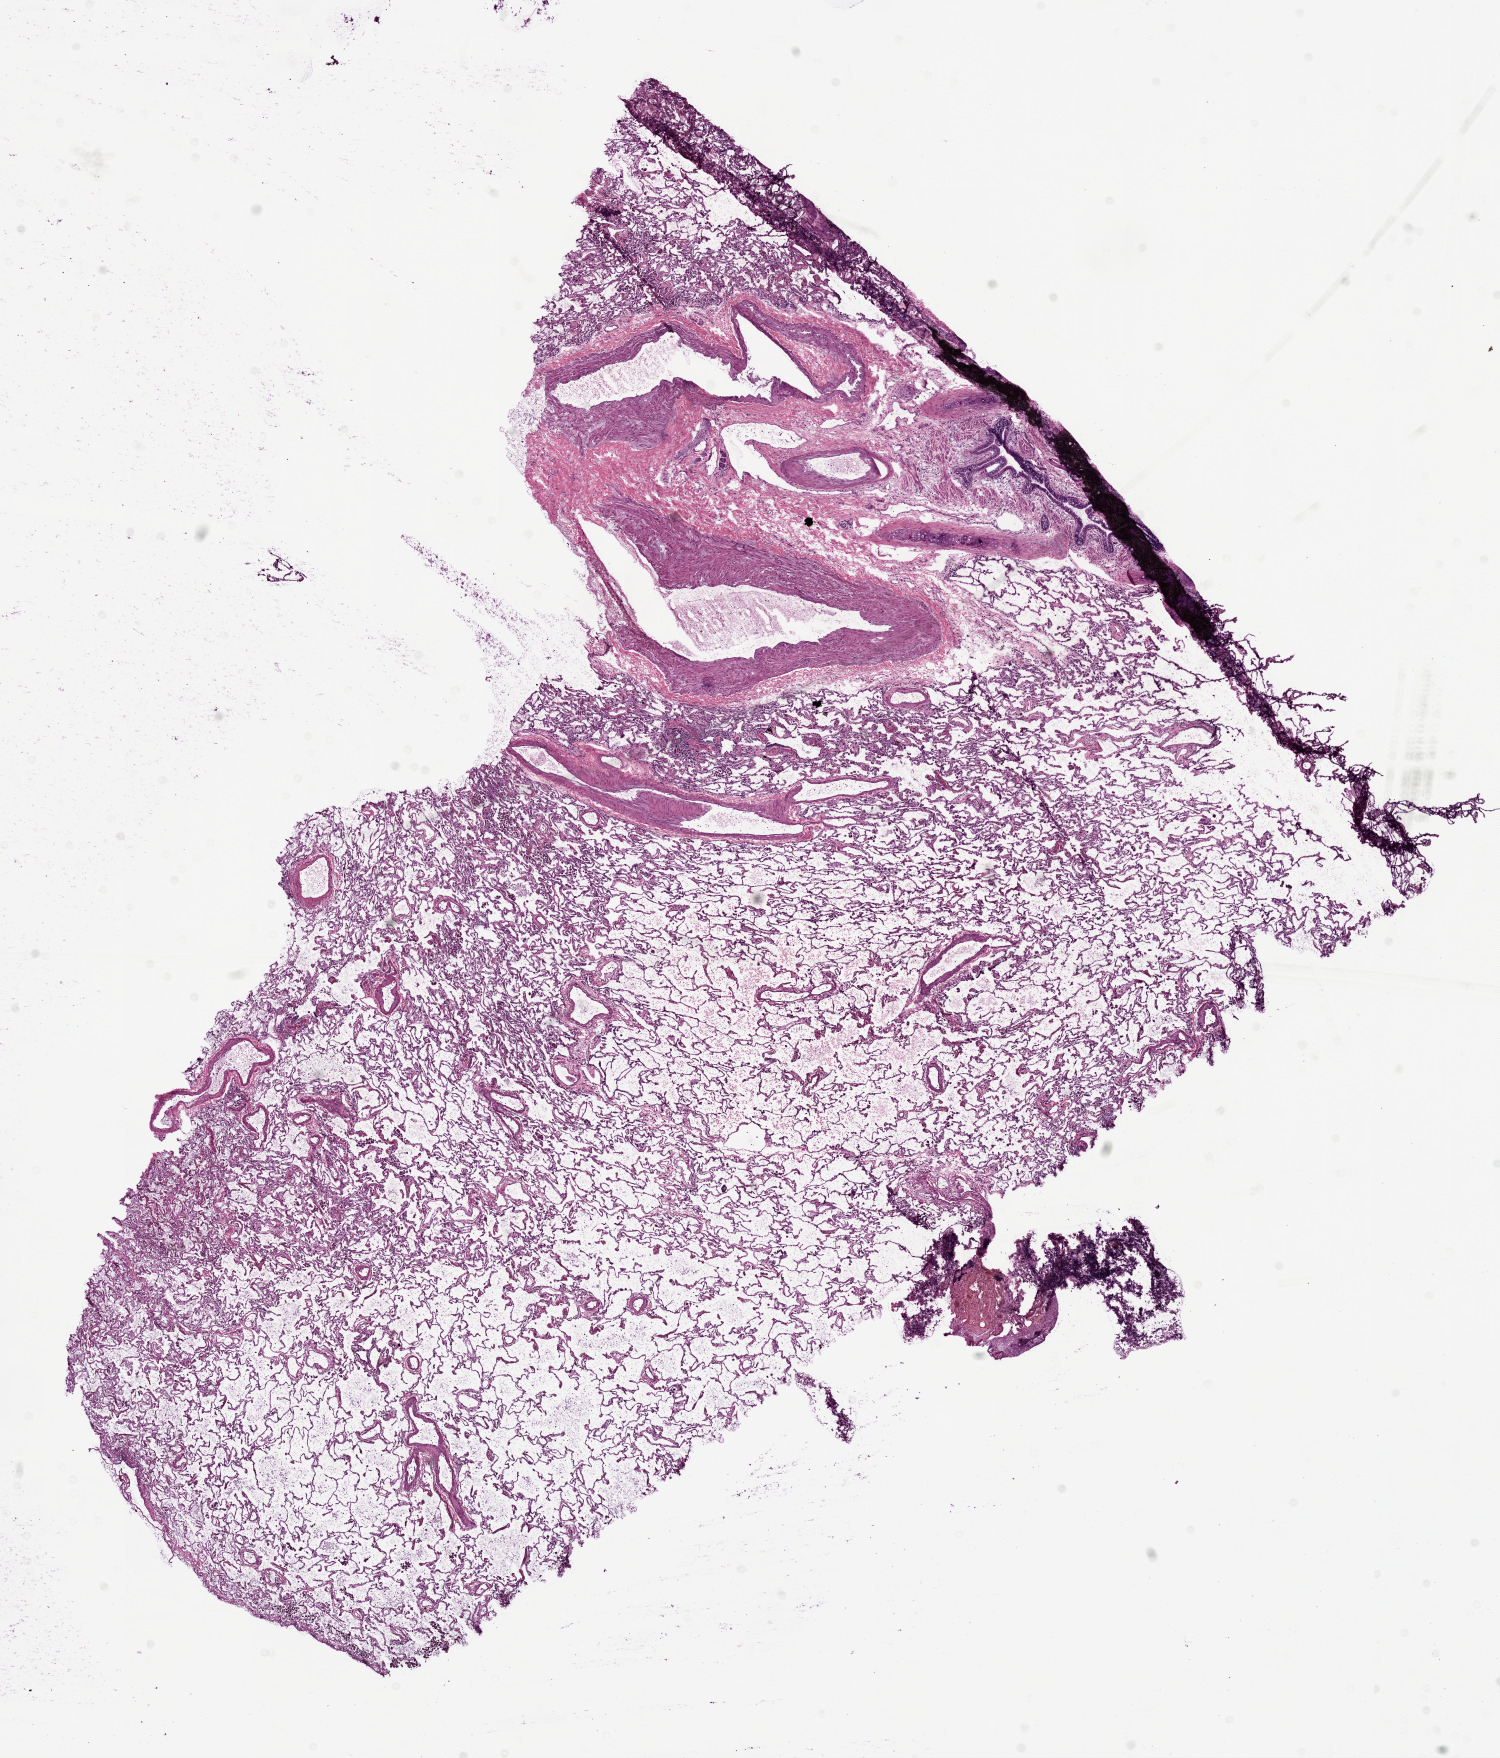
Digitized H&E tissue section (whole slide) — shown as a low-resolution overview of the whole scanned area (about 12.0 x 14.1 mm, slide scanned at 20x), frozen section from the top of the tissue portion, solid tissue normal (non-tumour tissue) sample from the lung. Female, age 67 years at initial diagnosis.
• this section: solid tissue normal (non-tumour) sample from the same patient
• patient diagnosis: Squamous cell carcinoma, NOS (upper lobe, lung)